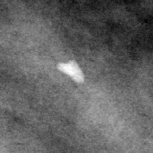
Cropped region of a digitized screen-film mammogram centred on a radiologist-marked abnormality, left breast, CC view.
Marked abnormality: calcifications, morphology vascular / coarse; BI-RADS assessment category 2; benign without callback (not worked up further).